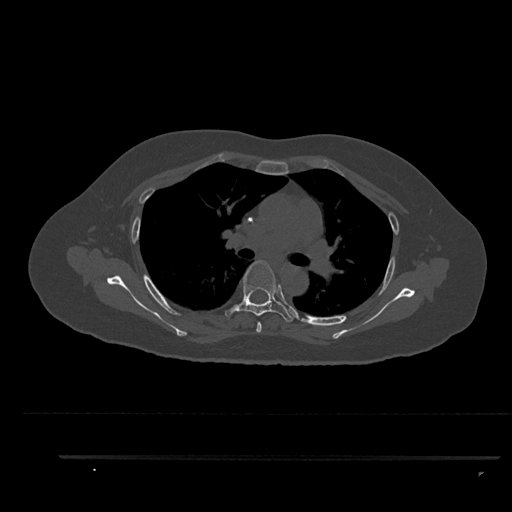
CT including the spine, one axial slice; slice 608 of 797 in the series (ordered by position); reconstruction kernel Br40s/3; 120 kVp; bone window (W 1800 / L 400 HU); 0.5 mm slice thickness; 512 × 512 image matrix, field of view 408 × 408 mm. Female patient, age 44 years. From the clinical record (not read from this slice): primary cancer: renal; vertebrae with lytic lesions (as recorded): L1.
Structures marked on this image (semi-automatically segmented with operator editing):
- T4 vertebra: bounding box <256,322,262,333> (left, top, right, bottom; pixels)
- T5 vertebra: <225,260,294,322>